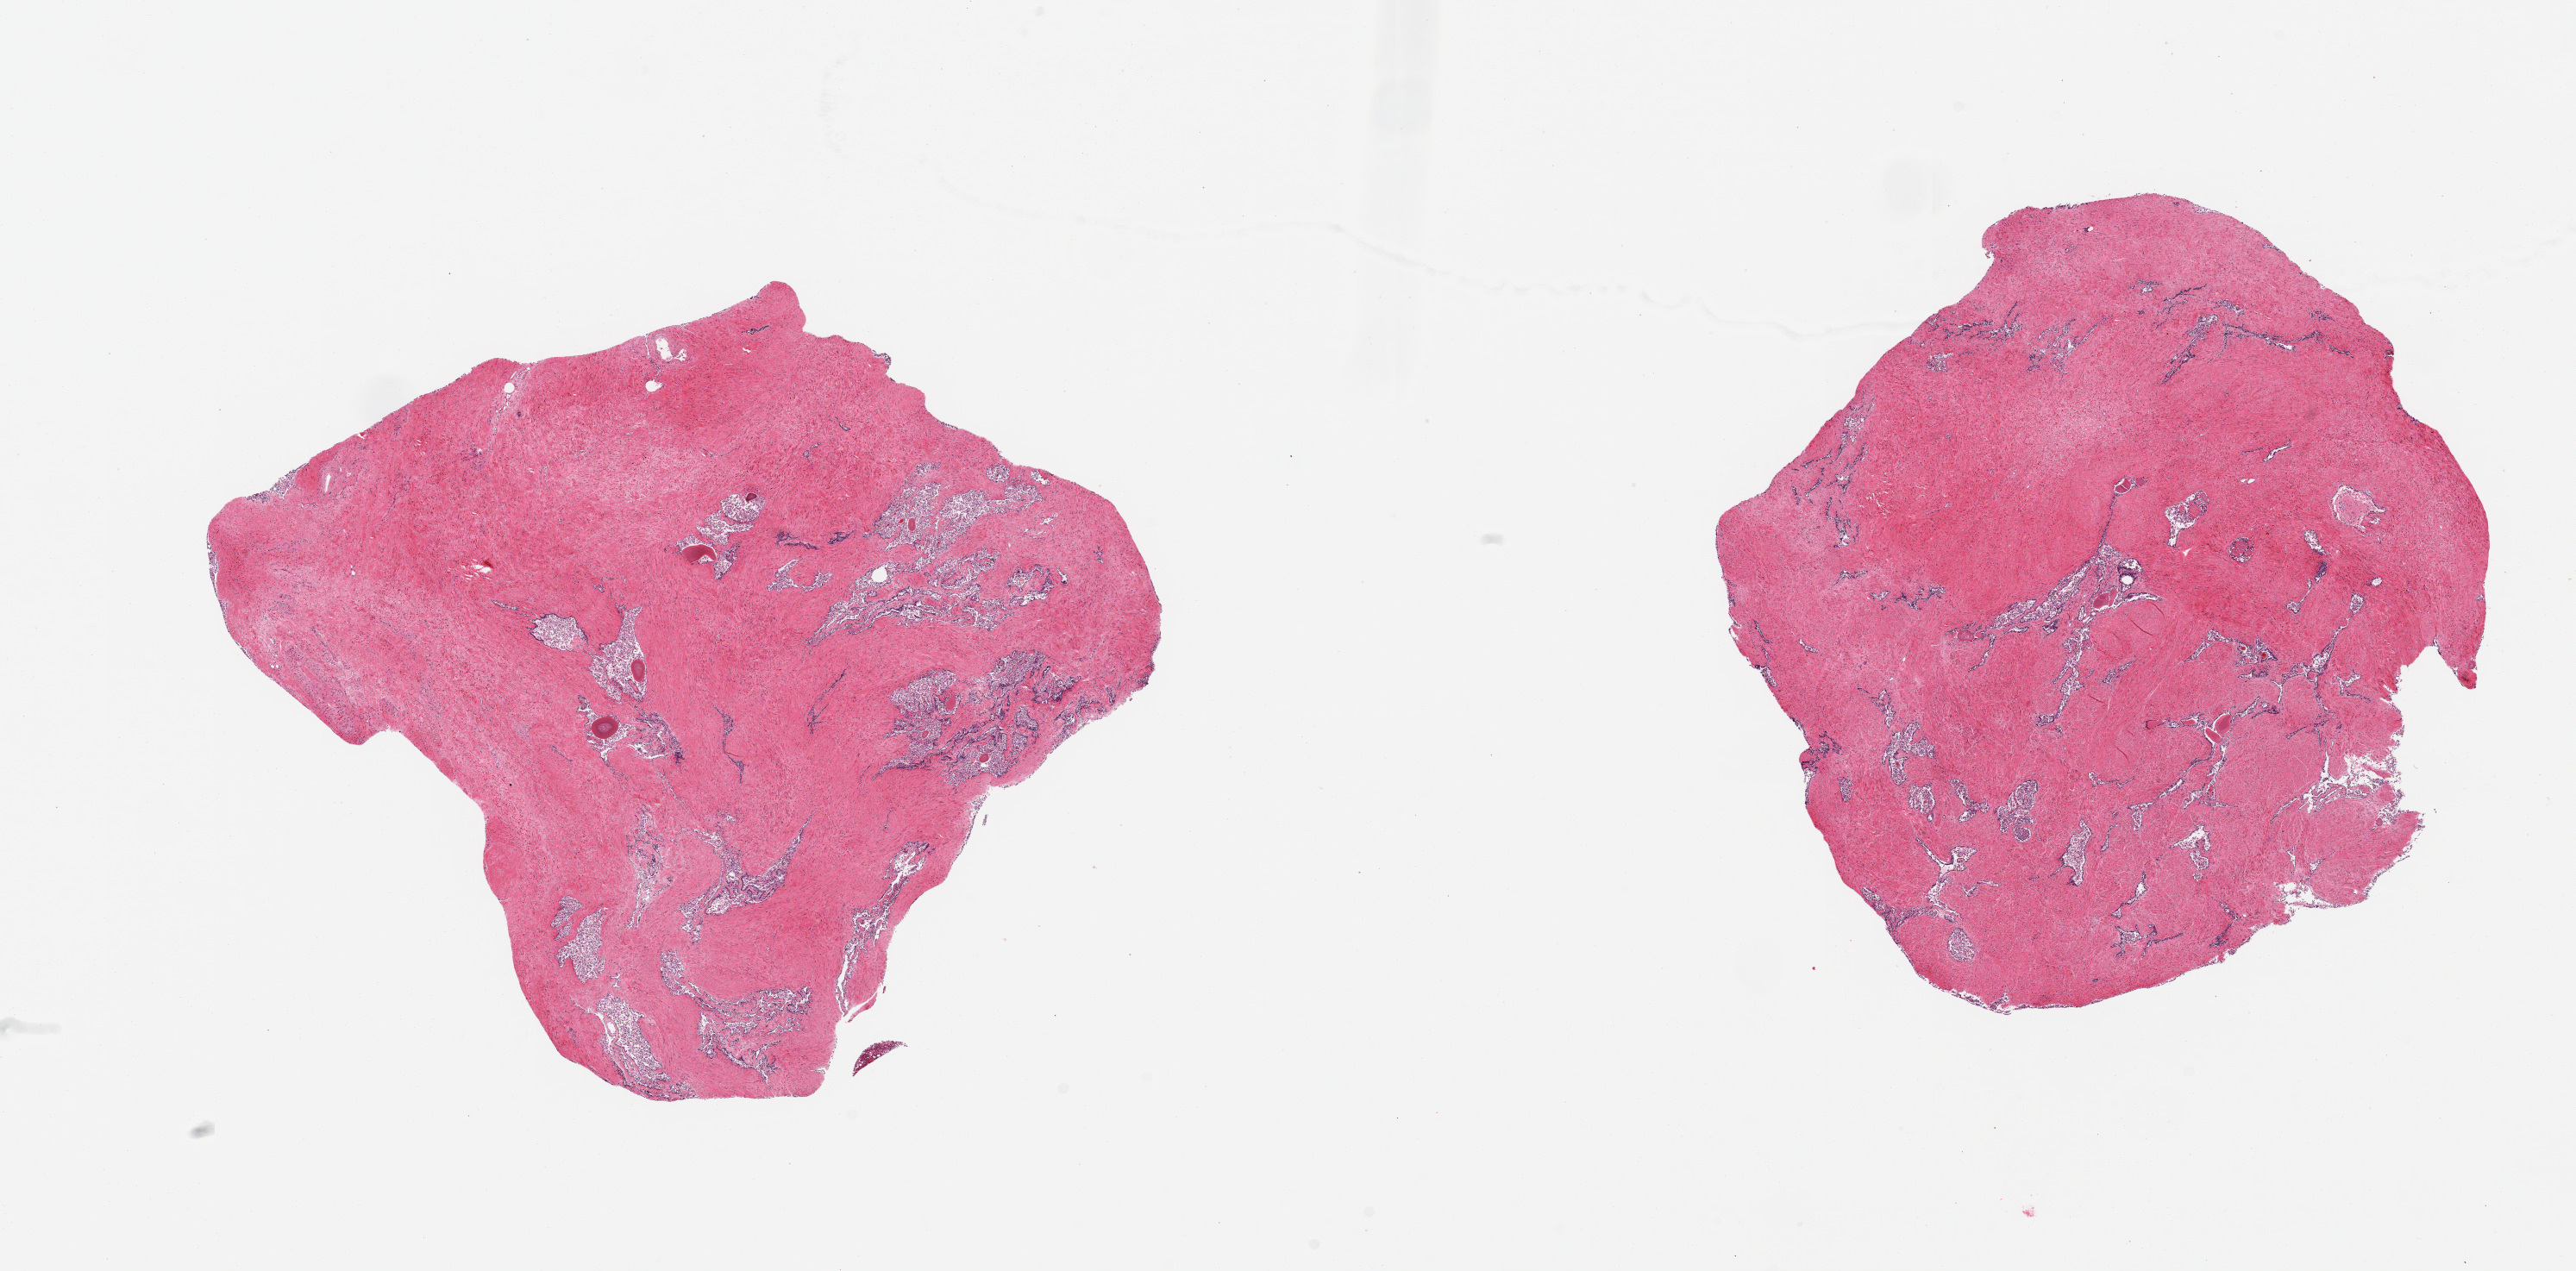
Haematoxylin and eosin whole-slide image — low-resolution overview of the scanned area, about 23.6 x 11.7 mm; PAXgene-fixed paraffin-embedded (PFPE) section; target tissue: prostate; donor tissue sample. Male donor.
Pathologist's review note for this sample: 2 pieces, glandular elements with advanced autolysis.